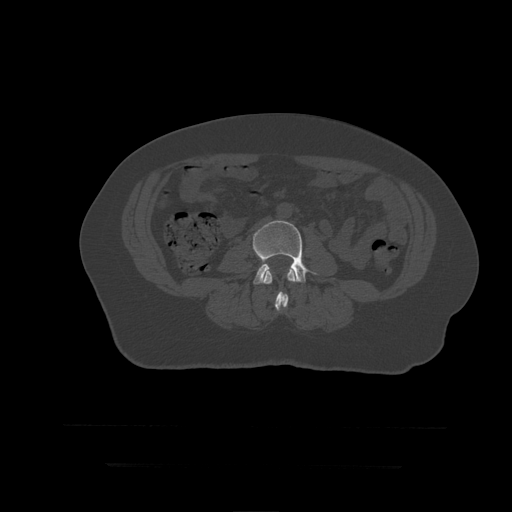
CT including the spine, one axial slice. Slice 107 of 399 in the series (ordered by position). Reconstruction kernel STANDARD. 120 kVp. Bone window (W 1800 / L 400 HU). 1.25 mm slice thickness. 512 × 512 image matrix, field of view 450 × 450 mm. Patient age 41 years. Case-level facts recorded for this patient, not image findings: primary cancer: breast.
Outlined on this slice (semi-automatically segmented with operator editing):
- L3 vertebra: bounding box (x1, y1, x2, y2) in pixels: (262, 265, 296, 312)
- L4 vertebra: (253, 221, 317, 285)